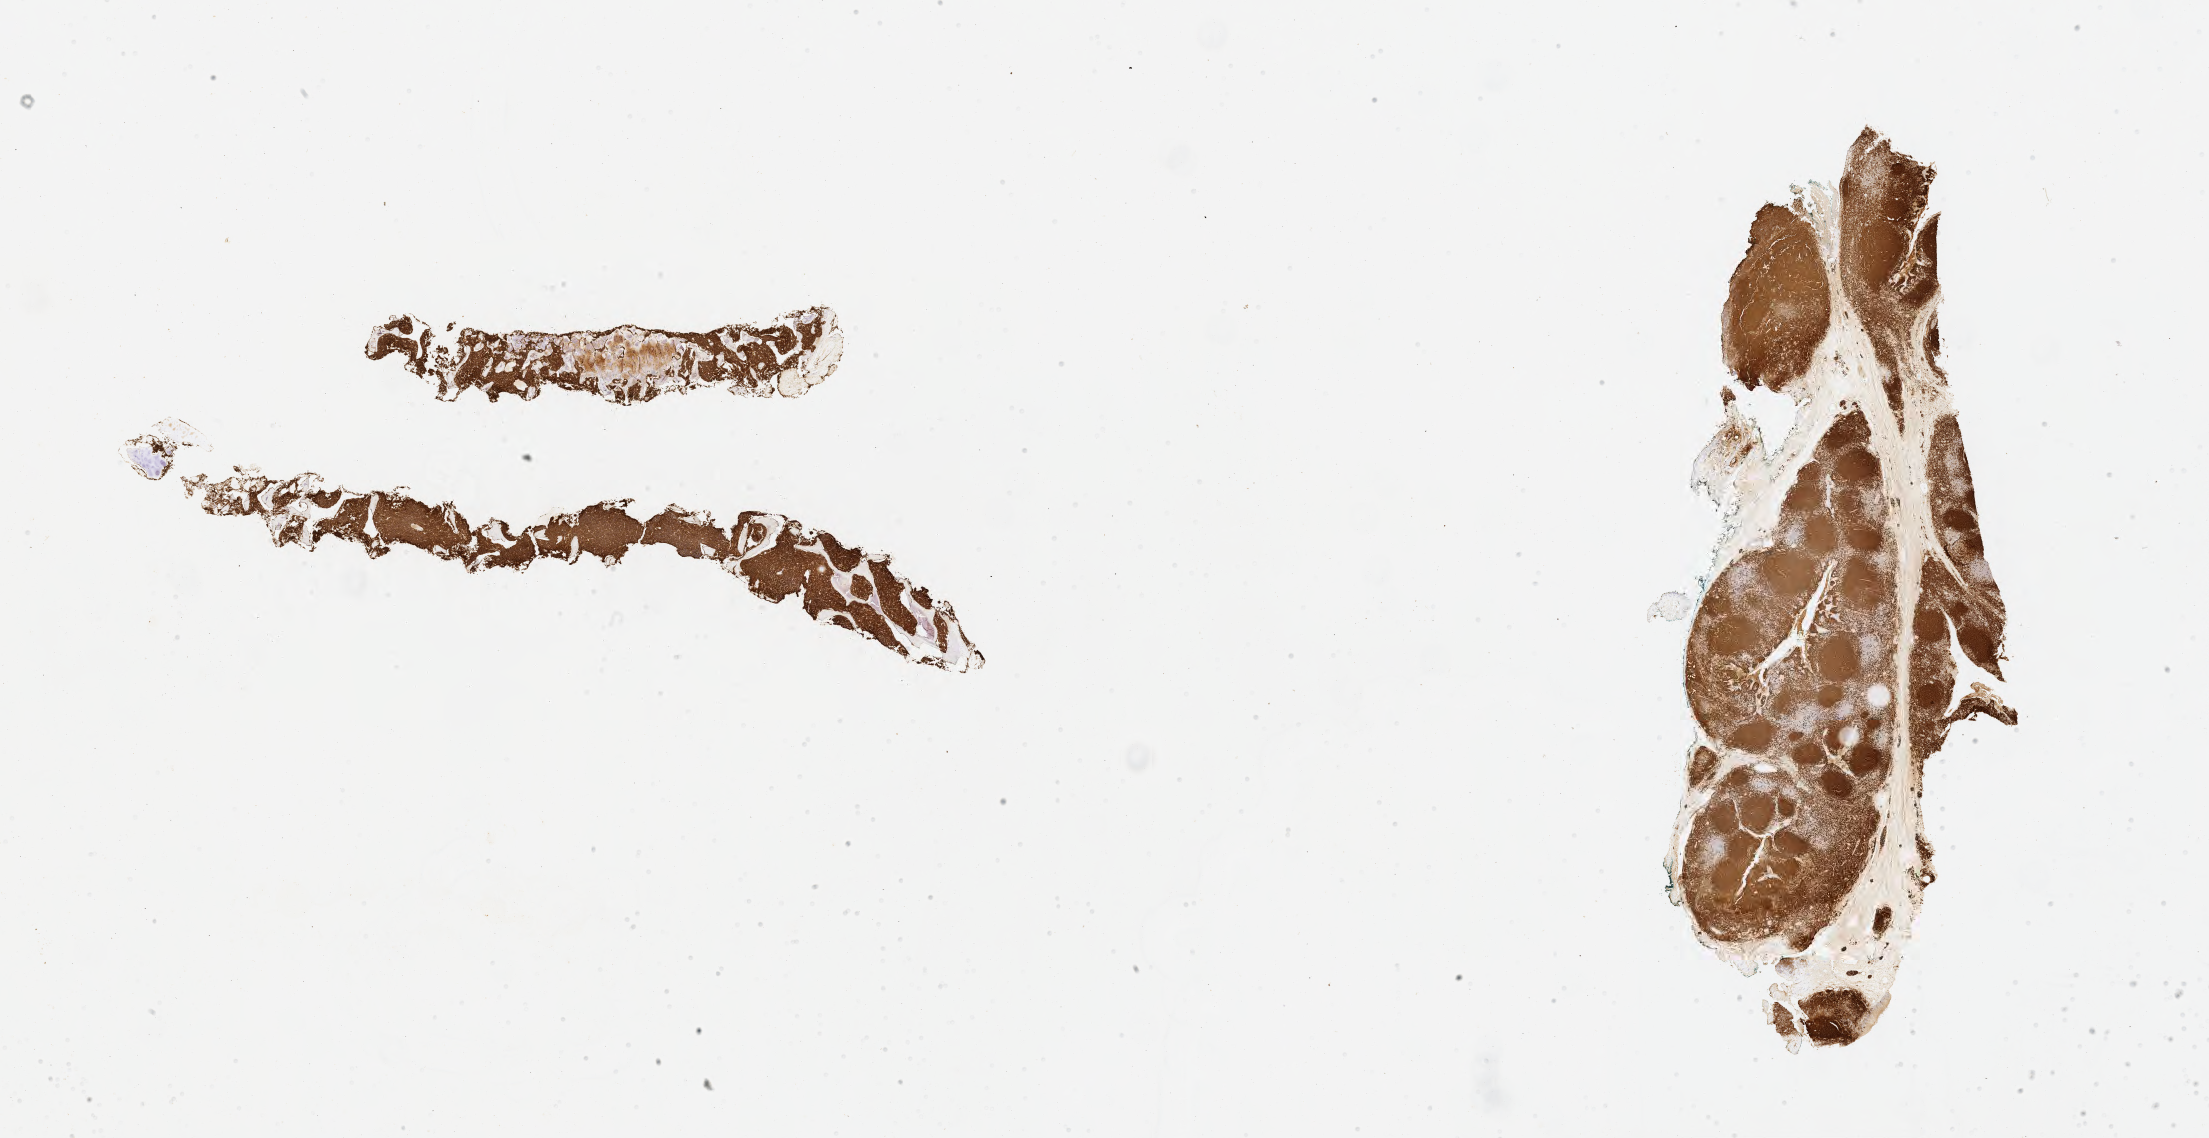
IHC for CD20, whole-slide image, a low-resolution overview of the entire scanned area, about 35.7 x 18.4 mm, specimen: tumor tissue, anatomic site: bone marrow. Male patient, age 11 years.
• diagnosis: Burkitt lymphoma, NOS